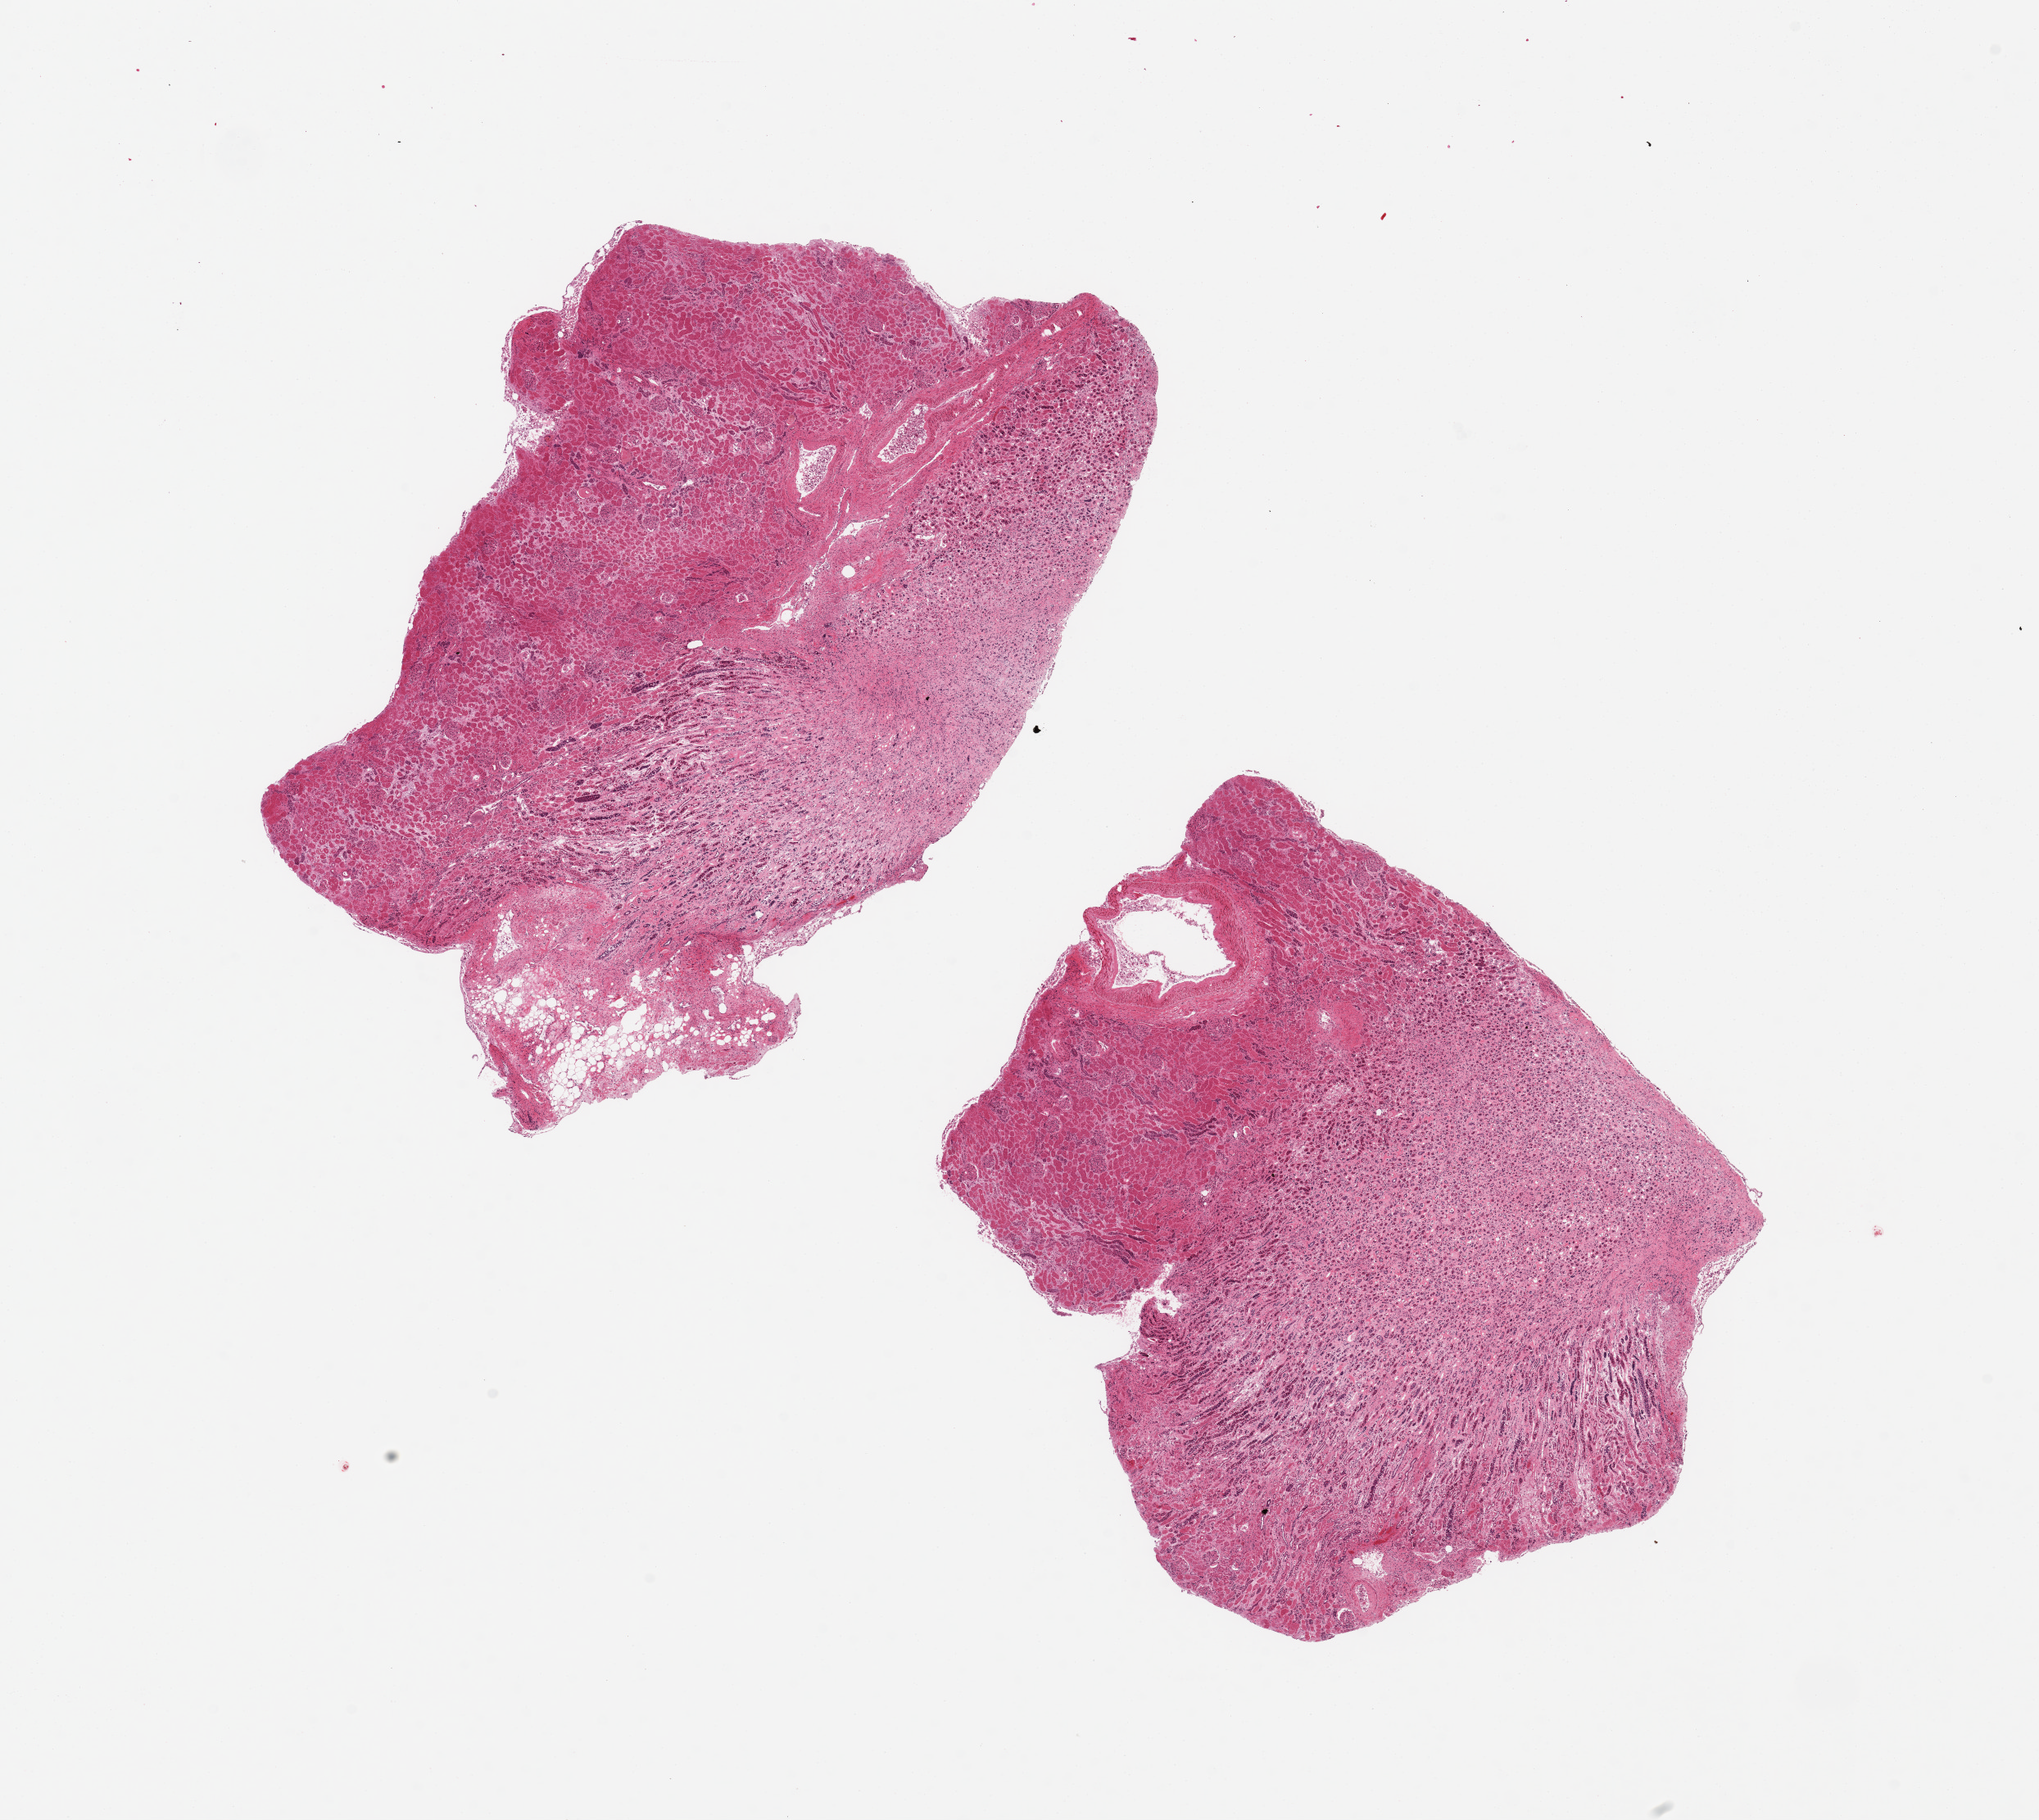
Whole-slide image, H&E stain, brightfield, a low-resolution overview of the entire scanned area, about 19.7 x 17.6 mm (acquisition: 20x scan). PAXgene-fixed paraffin-embedded (PFPE) section. Sampled site (target tissue): renal medulla. Tissue donor sample. Donor: male.
Review note (as recorded): 2 pieces, 9.5x5.3 & 8x6mm; each piece has half cortex, half medulla.